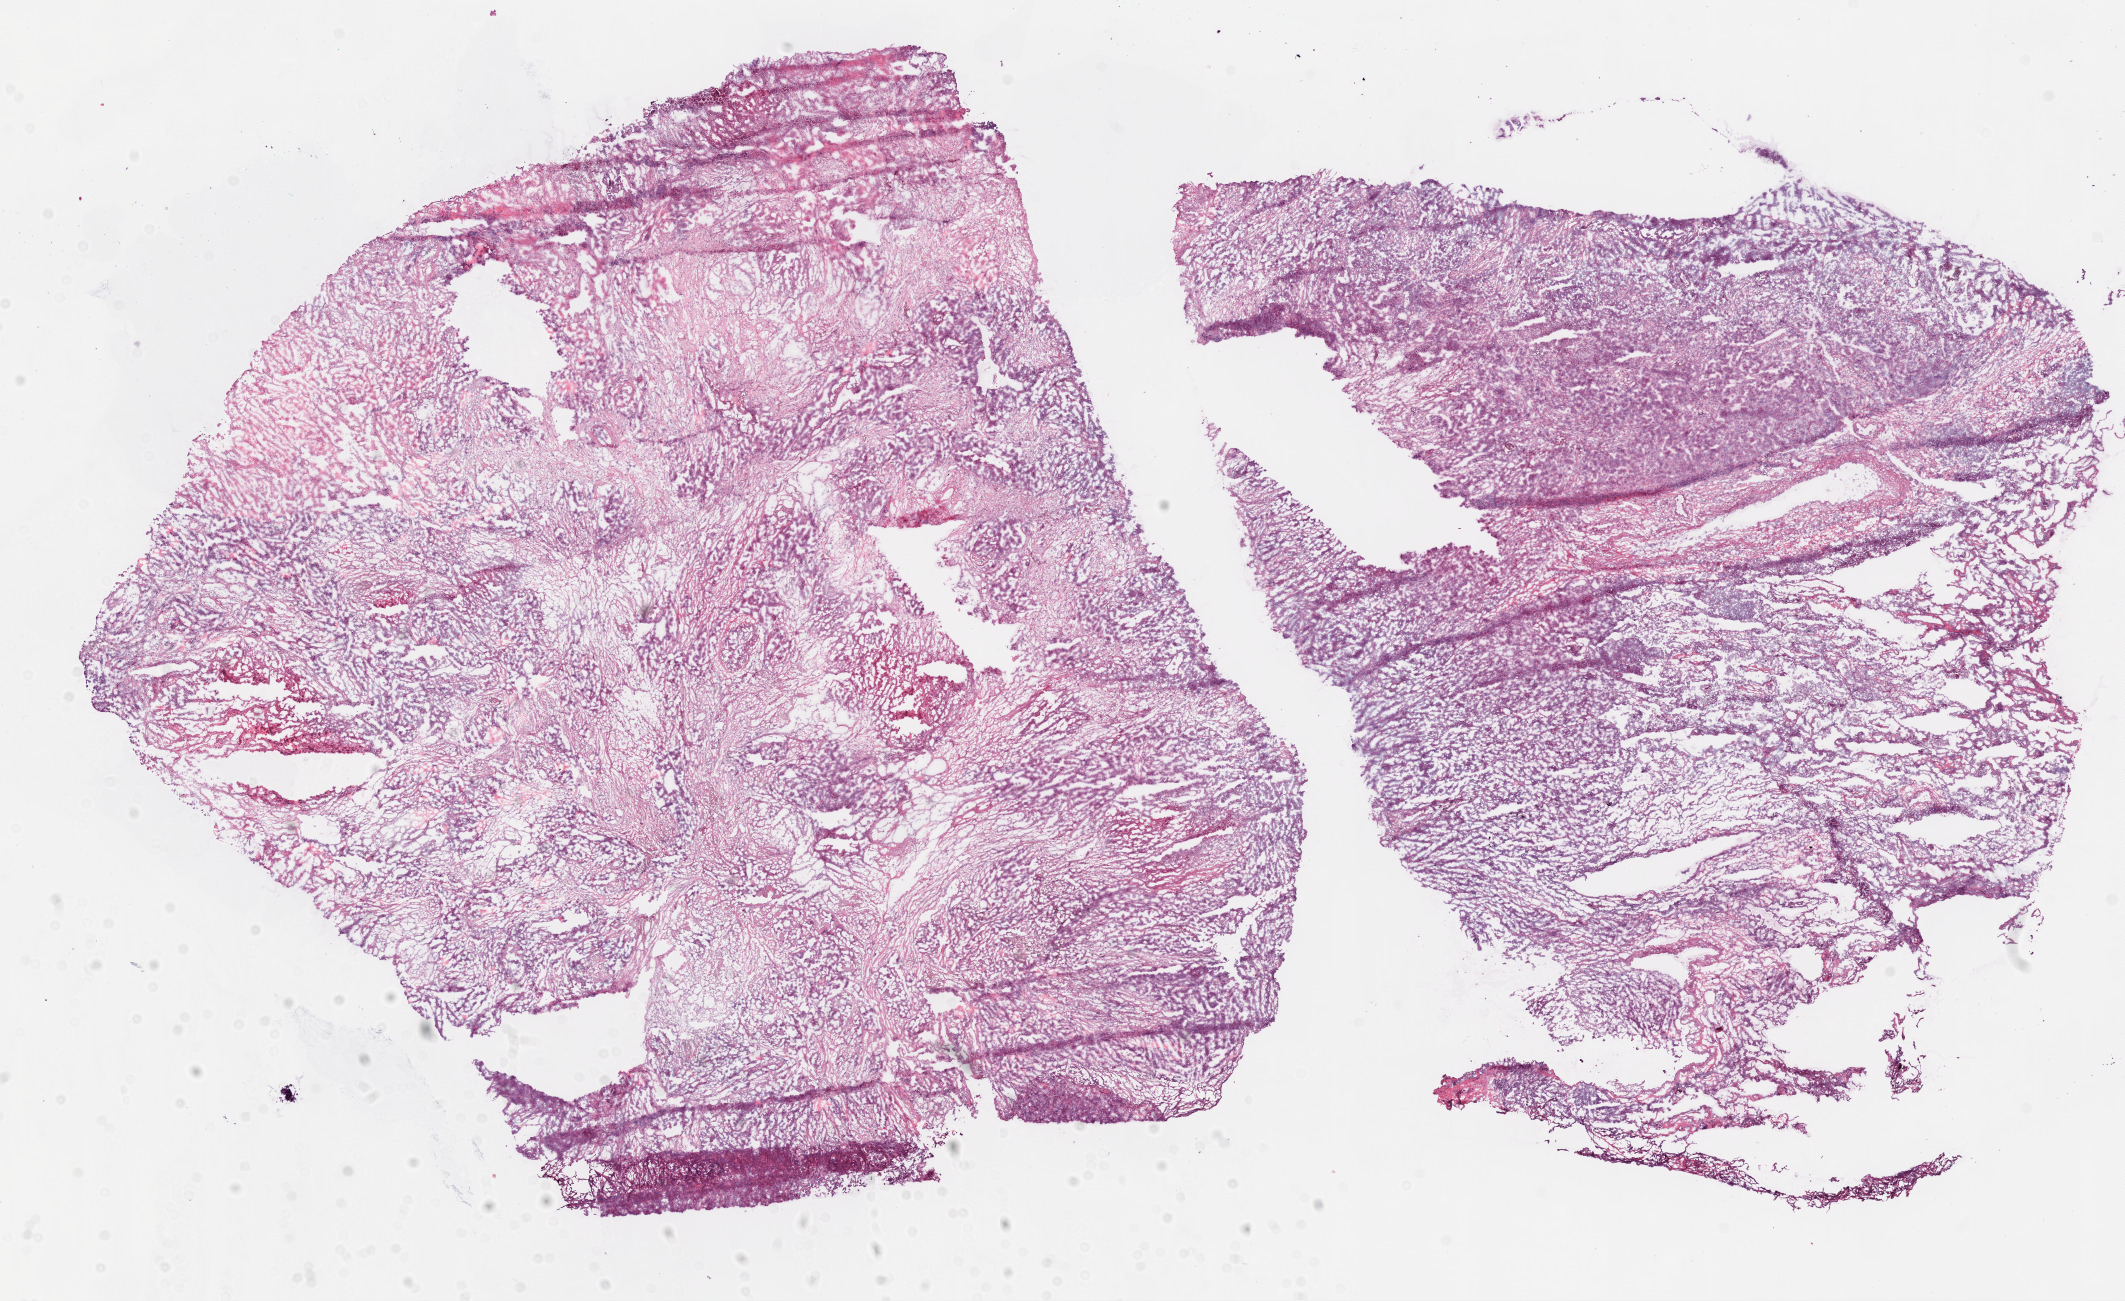
H&E whole-slide image, whole scanned area (about 17.1 x 10.4 mm) shown as a low-resolution overview; frozen section from the bottom of the tissue portion; sample: primary tumour, lung. Male, age 58 years at initial diagnosis. Slide review estimates, as recorded: tumour cells 50%, tumour nuclei 85%, normal cells 0%, stromal cells 47%, necrosis 3%.
• diagnosis: Adenocarcinoma, NOS (lower lobe, lung)
• laterality: right
• TNM: T1a N0 M0
• AJCC pathologic stage: IA